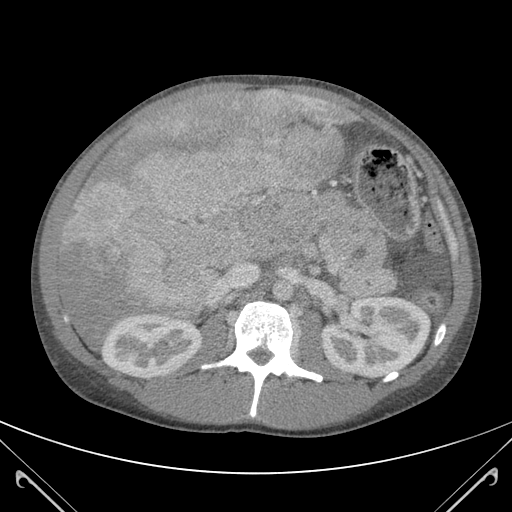
Contrast-enhanced abdominal CT (liver protocol), one axial slice. Slice 62 of 118 in the series (ordered by position). Soft-tissue window (W 400 / L 40 HU). 512 × 512 image matrix. From the clinical record (not read from this slice): diagnosis: hepatocellular carcinoma (patient treated with transarterial chemoembolisation; whether this scan precedes or follows treatment is not stated here); TNM stage (as recorded): Stage-IIIB; Child-Pugh class: A; tumour nodularity: uninodular.
Outlined on this slice (semi-automatic segmentation, software-assisted and operator-edited):
- abdominal aorta: bounding box (x1, y1, x2, y2) in pixels: (273, 280, 292, 301)
- liver parenchyma outside the tumour (the mass and vessels are separate outlines, so this box may not span the whole liver): (56, 89, 353, 348)
- mass: (68, 92, 339, 323)
- liver vessels: (207, 90, 327, 304)